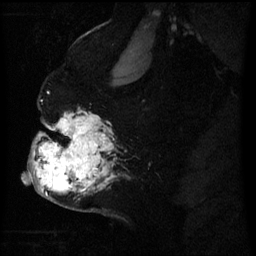
Breast MRI (dynamic contrast-enhanced), one sagittal slice. Position 41 of 60 along the scan axis. Dynamic contrast-enhanced series, image 2 of 3 at this slice position (ordered by acquisition). 1.5 T. TE 4.2 ms, TR 8 ms. 256 × 256 image matrix, field of view 200 × 200 mm. Female patient, age 50 years.
Annotated regions visible in this slice (semi-automatically segmented with operator editing):
- analysis volume of interest (the breast-tissue region the enhancement analysis was run in; not a lesion): bounding box (x1, y1, x2, y2) in pixels: (32, 120, 107, 201)
- tumour enhancement mask (voxels above the 70 % enhancement threshold inside the analysis volume of interest): (35, 122, 105, 191)